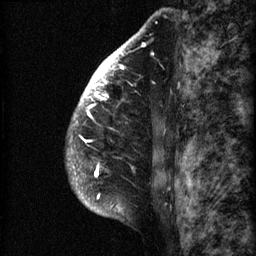
Breast MRI (dynamic contrast-enhanced), one sagittal slice. 3 images stored at this slice position (order not interpretable as contrast timing). 1.5 T. TE 4.2 ms, TR 22.7 ms. 2 mm slice thickness. 256 × 256 image matrix, field of view 180 × 180 mm. Patient: female, 48 years. From the clinical record (not read from this slice): setting: breast cancer imaged before/during neoadjuvant chemotherapy; receptor status: triple-negative.
Annotated regions visible in this slice (semi-automatically segmented with operator editing):
- analysis volume of interest (the breast-tissue region the enhancement analysis was run in; not a lesion): bounding box (x1, y1, x2, y2) in pixels: (66, 30, 173, 207)
- tumour enhancement mask (voxels above the 90 % enhancement threshold inside the analysis volume of interest): (68, 33, 142, 199)